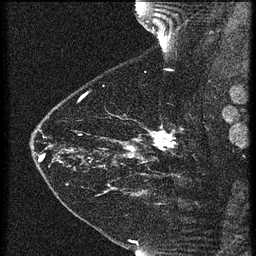
Breast MRI (dynamic contrast-enhanced), one sagittal slice. 3 images stored at this slice position (order not interpretable as contrast timing). 1.5 T. TE 4.2 ms, TR 21.3 ms. 1.5 mm slice thickness. 256 × 256 image matrix, field of view 180 × 180 mm. Female patient, age 43 years. From the clinical record (not read from this slice): setting: breast cancer imaged before/during neoadjuvant chemotherapy; receptor status: HER2-positive.
Structures marked on this image (semi-automatic segmentation, software-assisted and operator-edited):
- analysis volume of interest (the breast-tissue region the enhancement analysis was run in; not a lesion): bounding box [x1, y1, x2, y2] px = [119, 114, 189, 173]
- tumour enhancement mask (voxels above the 90 % enhancement threshold inside the analysis volume of interest): [126, 130, 176, 159]